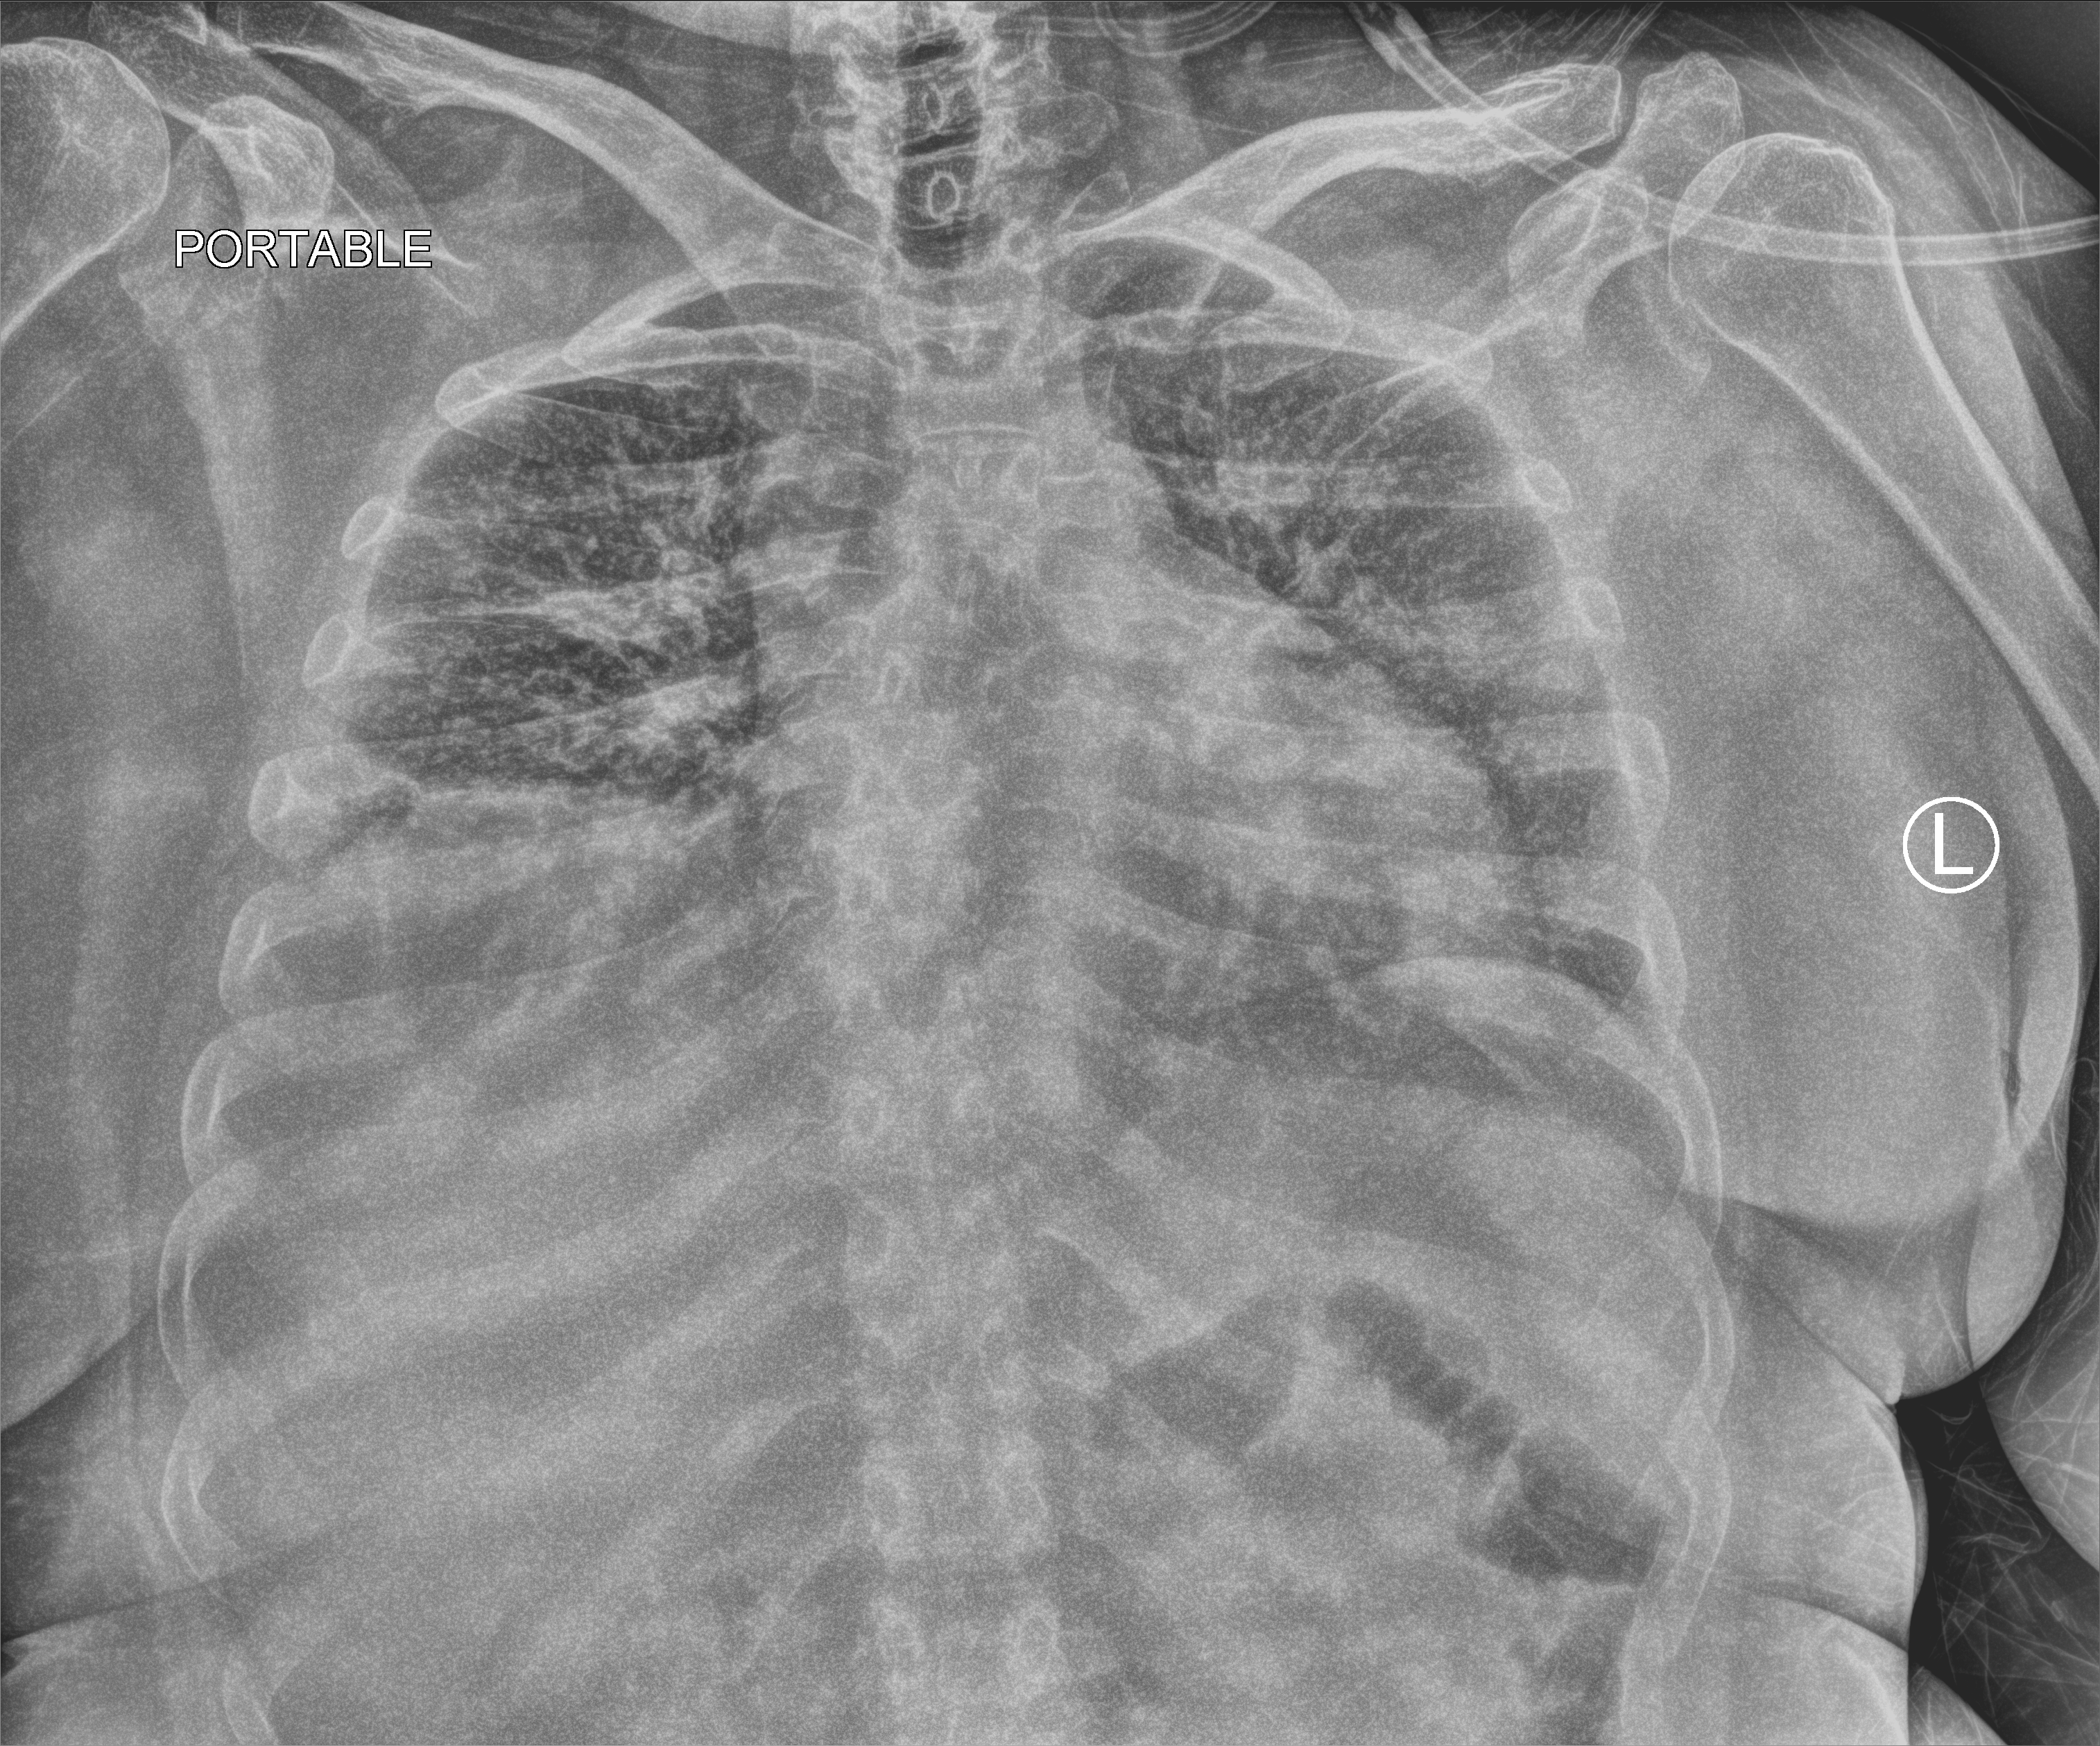
Portable chest radiograph, anteroposterior (AP) projection. Female patient hospitalised with COVID-19, age 18–59 years.
From the hospital-stay record, not from the radiograph (when in the stay this image was taken is not recorded):
- admitted to intensive care during this hospital stay: no